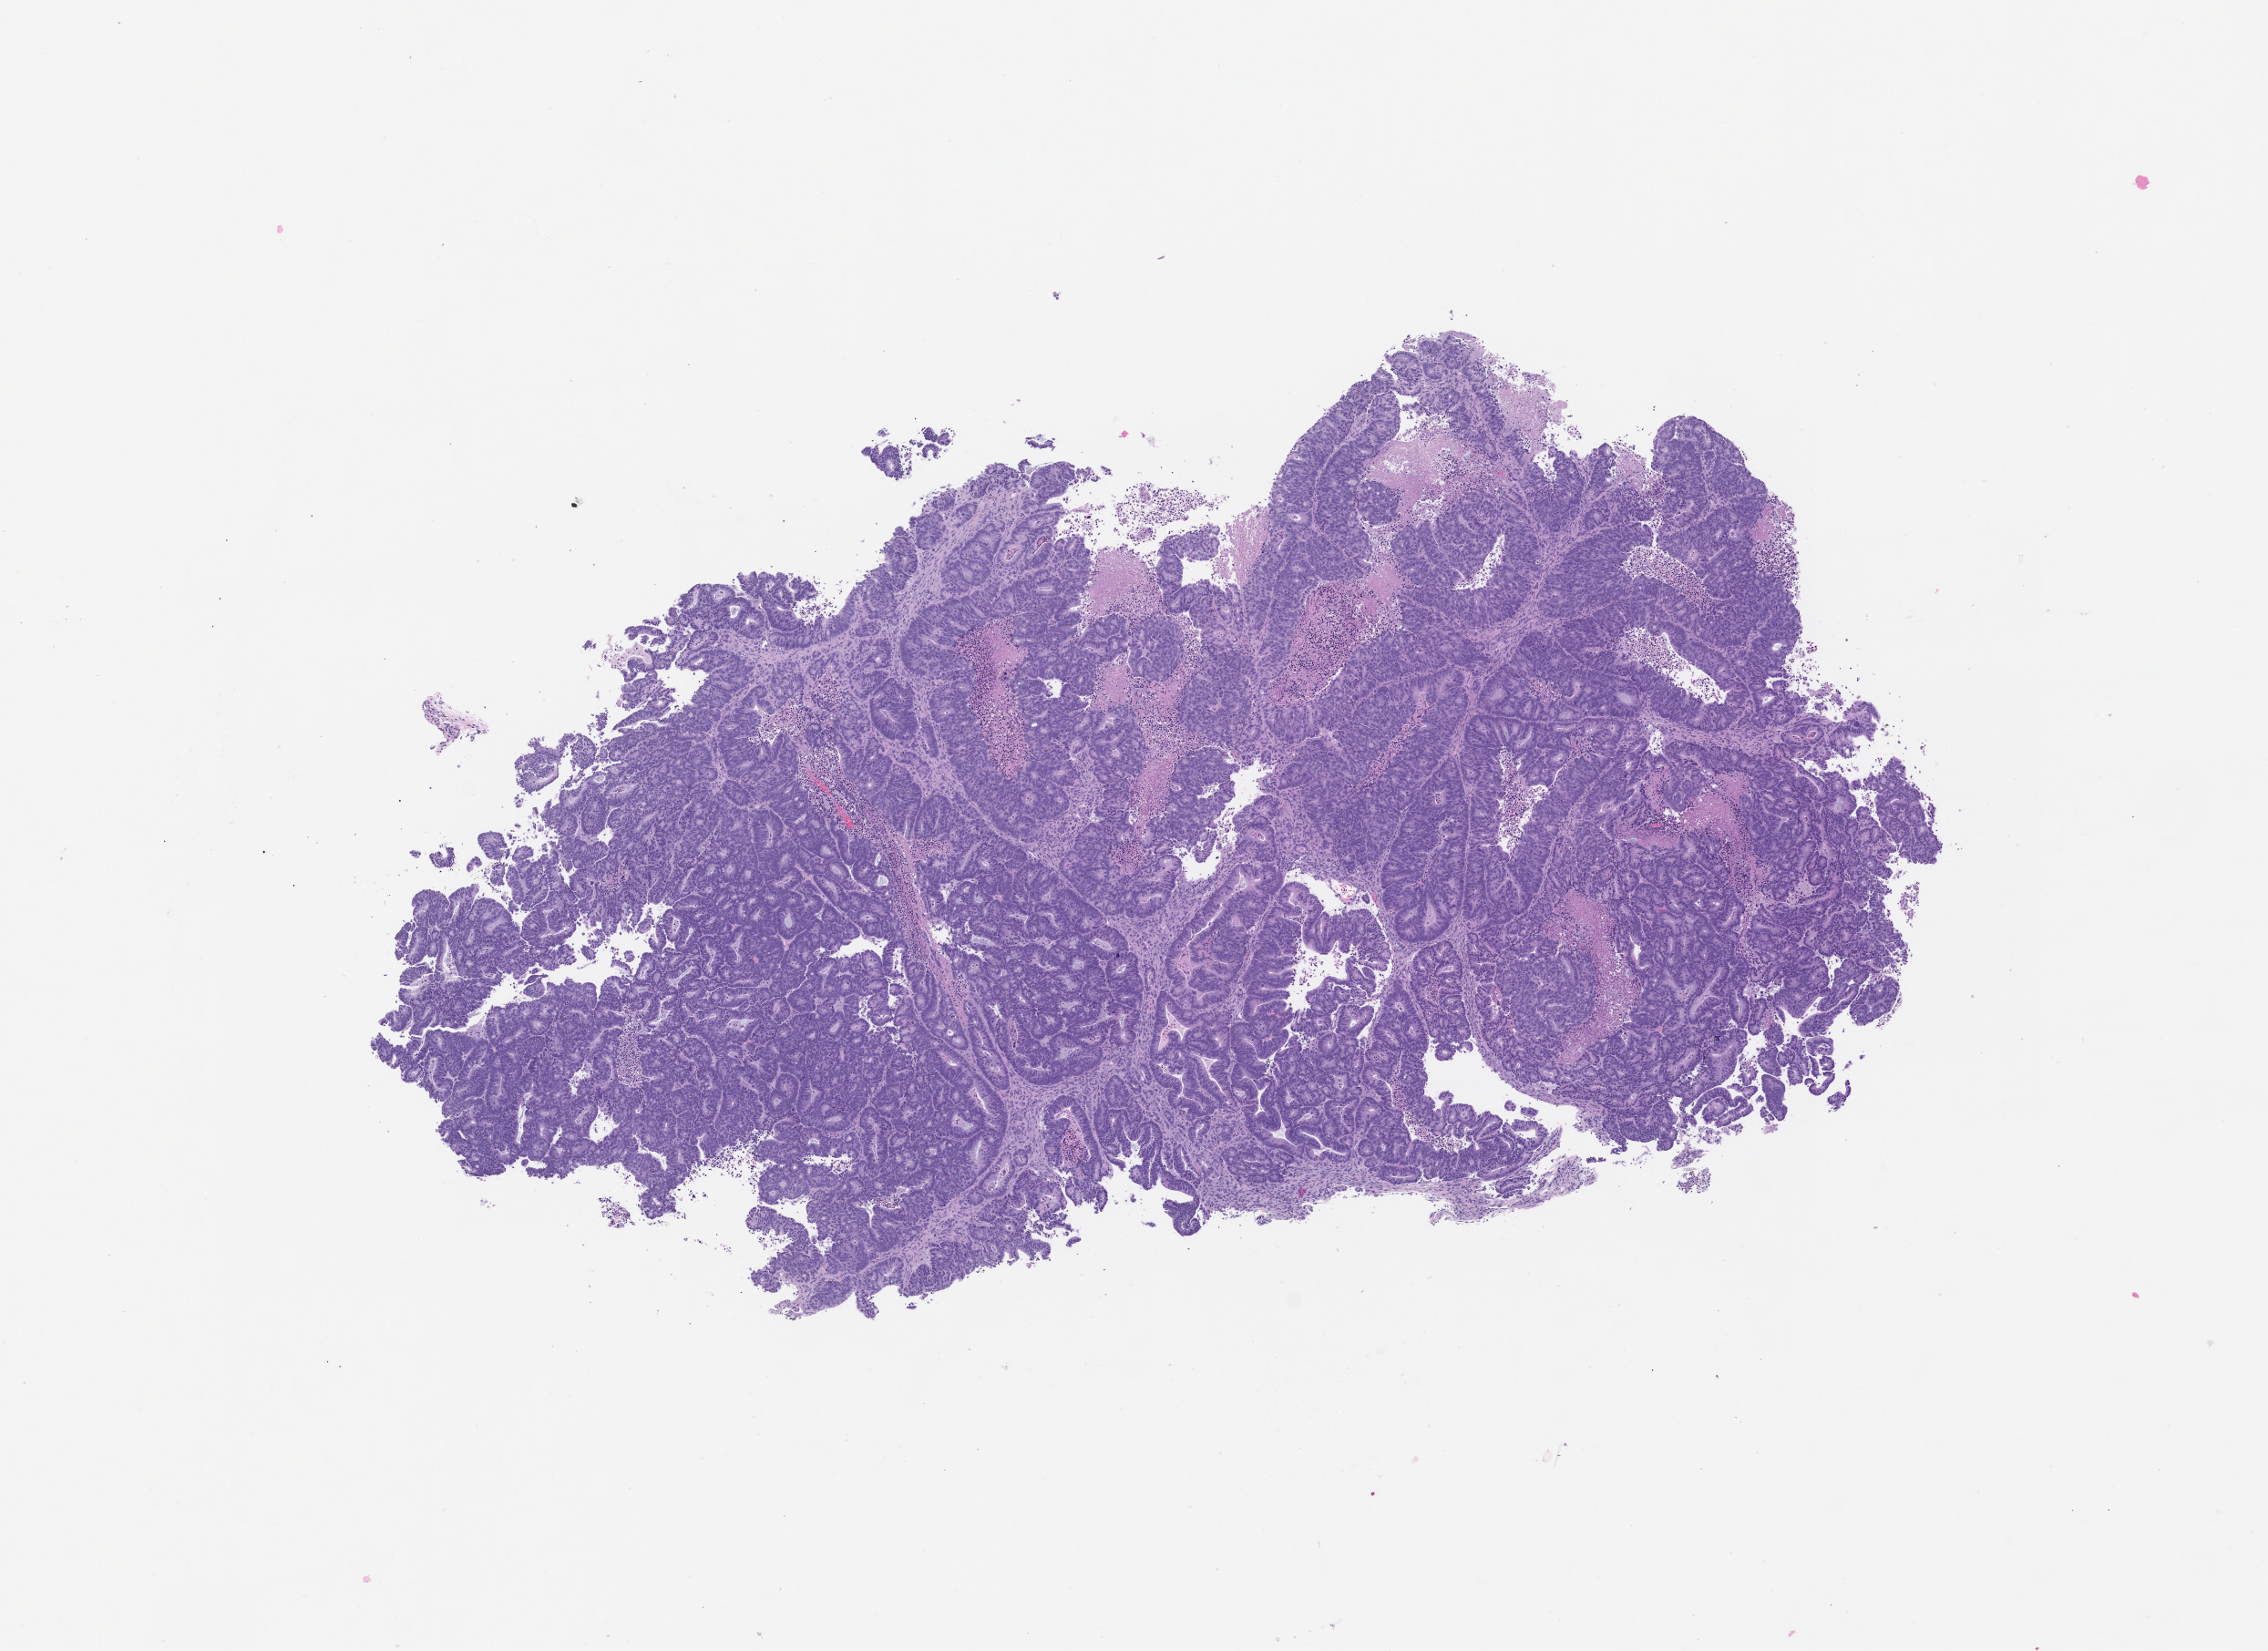
Hematoxylin and eosin (H&E) whole-slide image of a patient-derived xenograft (PDX) tumor grown in a mouse, passage 0, shown as a low-resolution overview of the whole scanned area (about 10.0 x 7.3 mm); formalin-fixed paraffin-embedded section; tumor site category: colon.
- originating patient diagnosis: Colon Adenocarcinoma